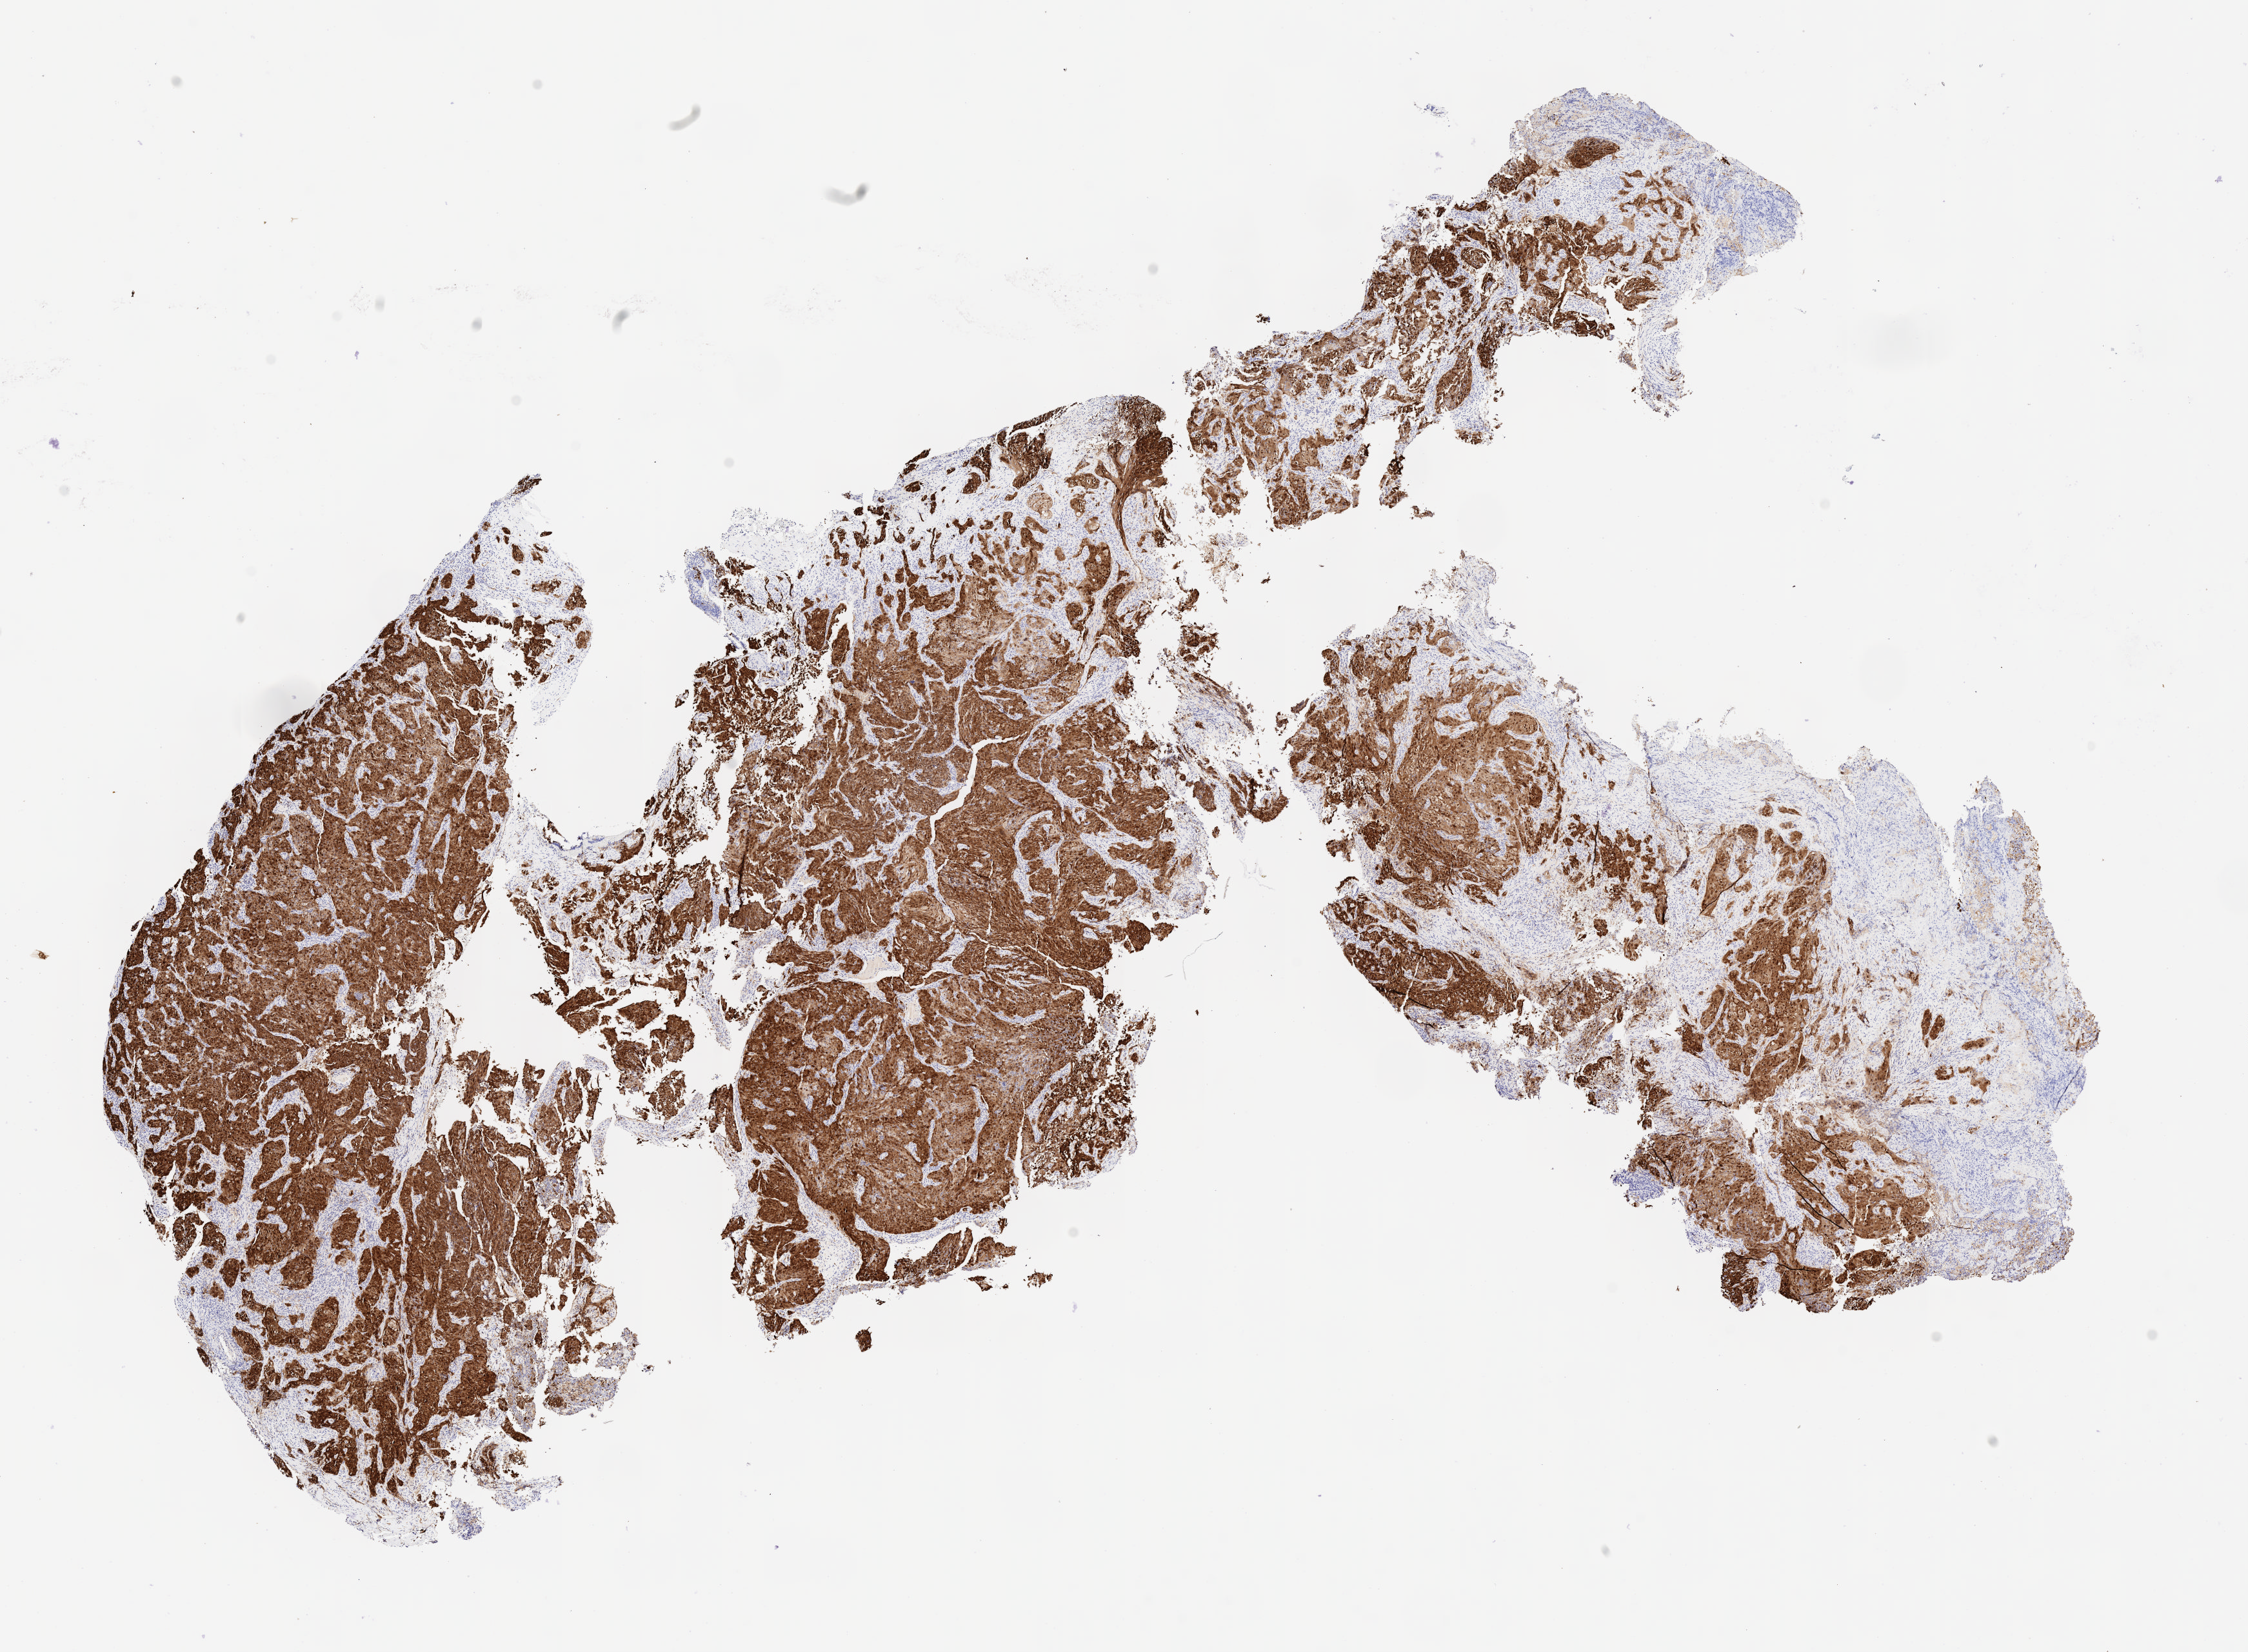
Whole-slide image, immunohistochemical stain for p16 (p16INK4a) — low-resolution overview of the scanned area, about 14.1 x 10.4 mm. Specimen: tumor tissue. Anatomic site: cervix. Patient: female, 54 years old.
Diagnosis: Adenocarcinoma, NOS.